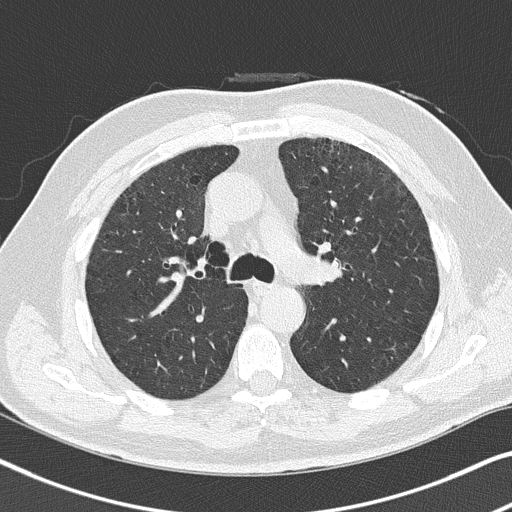
Axial slice from a low-dose chest CT screening exam. Baseline screening round. Lung window (W 1500 / L -600 HU). Slice 110 of 300 in the series. Male, age 64 years at enrolment. Current smoker at enrolment.
Expert-annotated lung lesion, bounding box (x1, y1, x2, y2) in pixels: (322, 247, 356, 276). Screening reader's record for this exam (one nodule recorded; not confirmed to be the boxed lesion): non-calcified nodule or mass ≥4 mm, left upper lobe, 4 × 4 mm, smooth margins, soft tissue attenuation. Lung cancer was diagnosed 450 days after this screen (after the second annual screen): squamous cell carcinoma, keratinizing, NOS, left upper lobe, moderately differentiated (G2), stage IA (AJCC 6th edition), 4 mm at pathology.